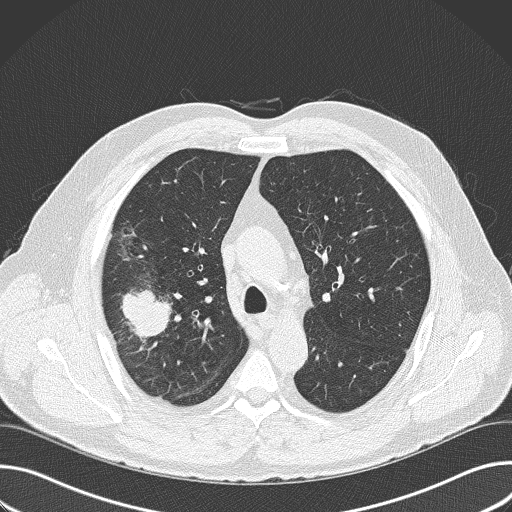
Axial slice from a low-dose chest CT screening exam, baseline annual screen, lung window (W 1500 / L -600 HU), 2 mm slice thickness, lung (sharp) reconstruction kernel (B50f), 120 kVp, slice 112 of 157 in the series. Male, age 56 years at enrolment.
Expert reader's lesion annotation, bounding box [x1, y1, x2, y2] px = [83, 268, 189, 379]. The exam's reader record, not a measurement of the box and not confirmed to be the same lesion: non-calcified nodule or mass ≥4 mm, right upper lobe, 6 × 5 mm, spiculated (stellate) margins, soft tissue attenuation. Participant outcome: lung cancer diagnosed 16 days after this screen — adenocarcinoma, NOS, right upper lobe, poorly differentiated (G3), stage IIB (AJCC 6th edition), 60 mm at pathology.